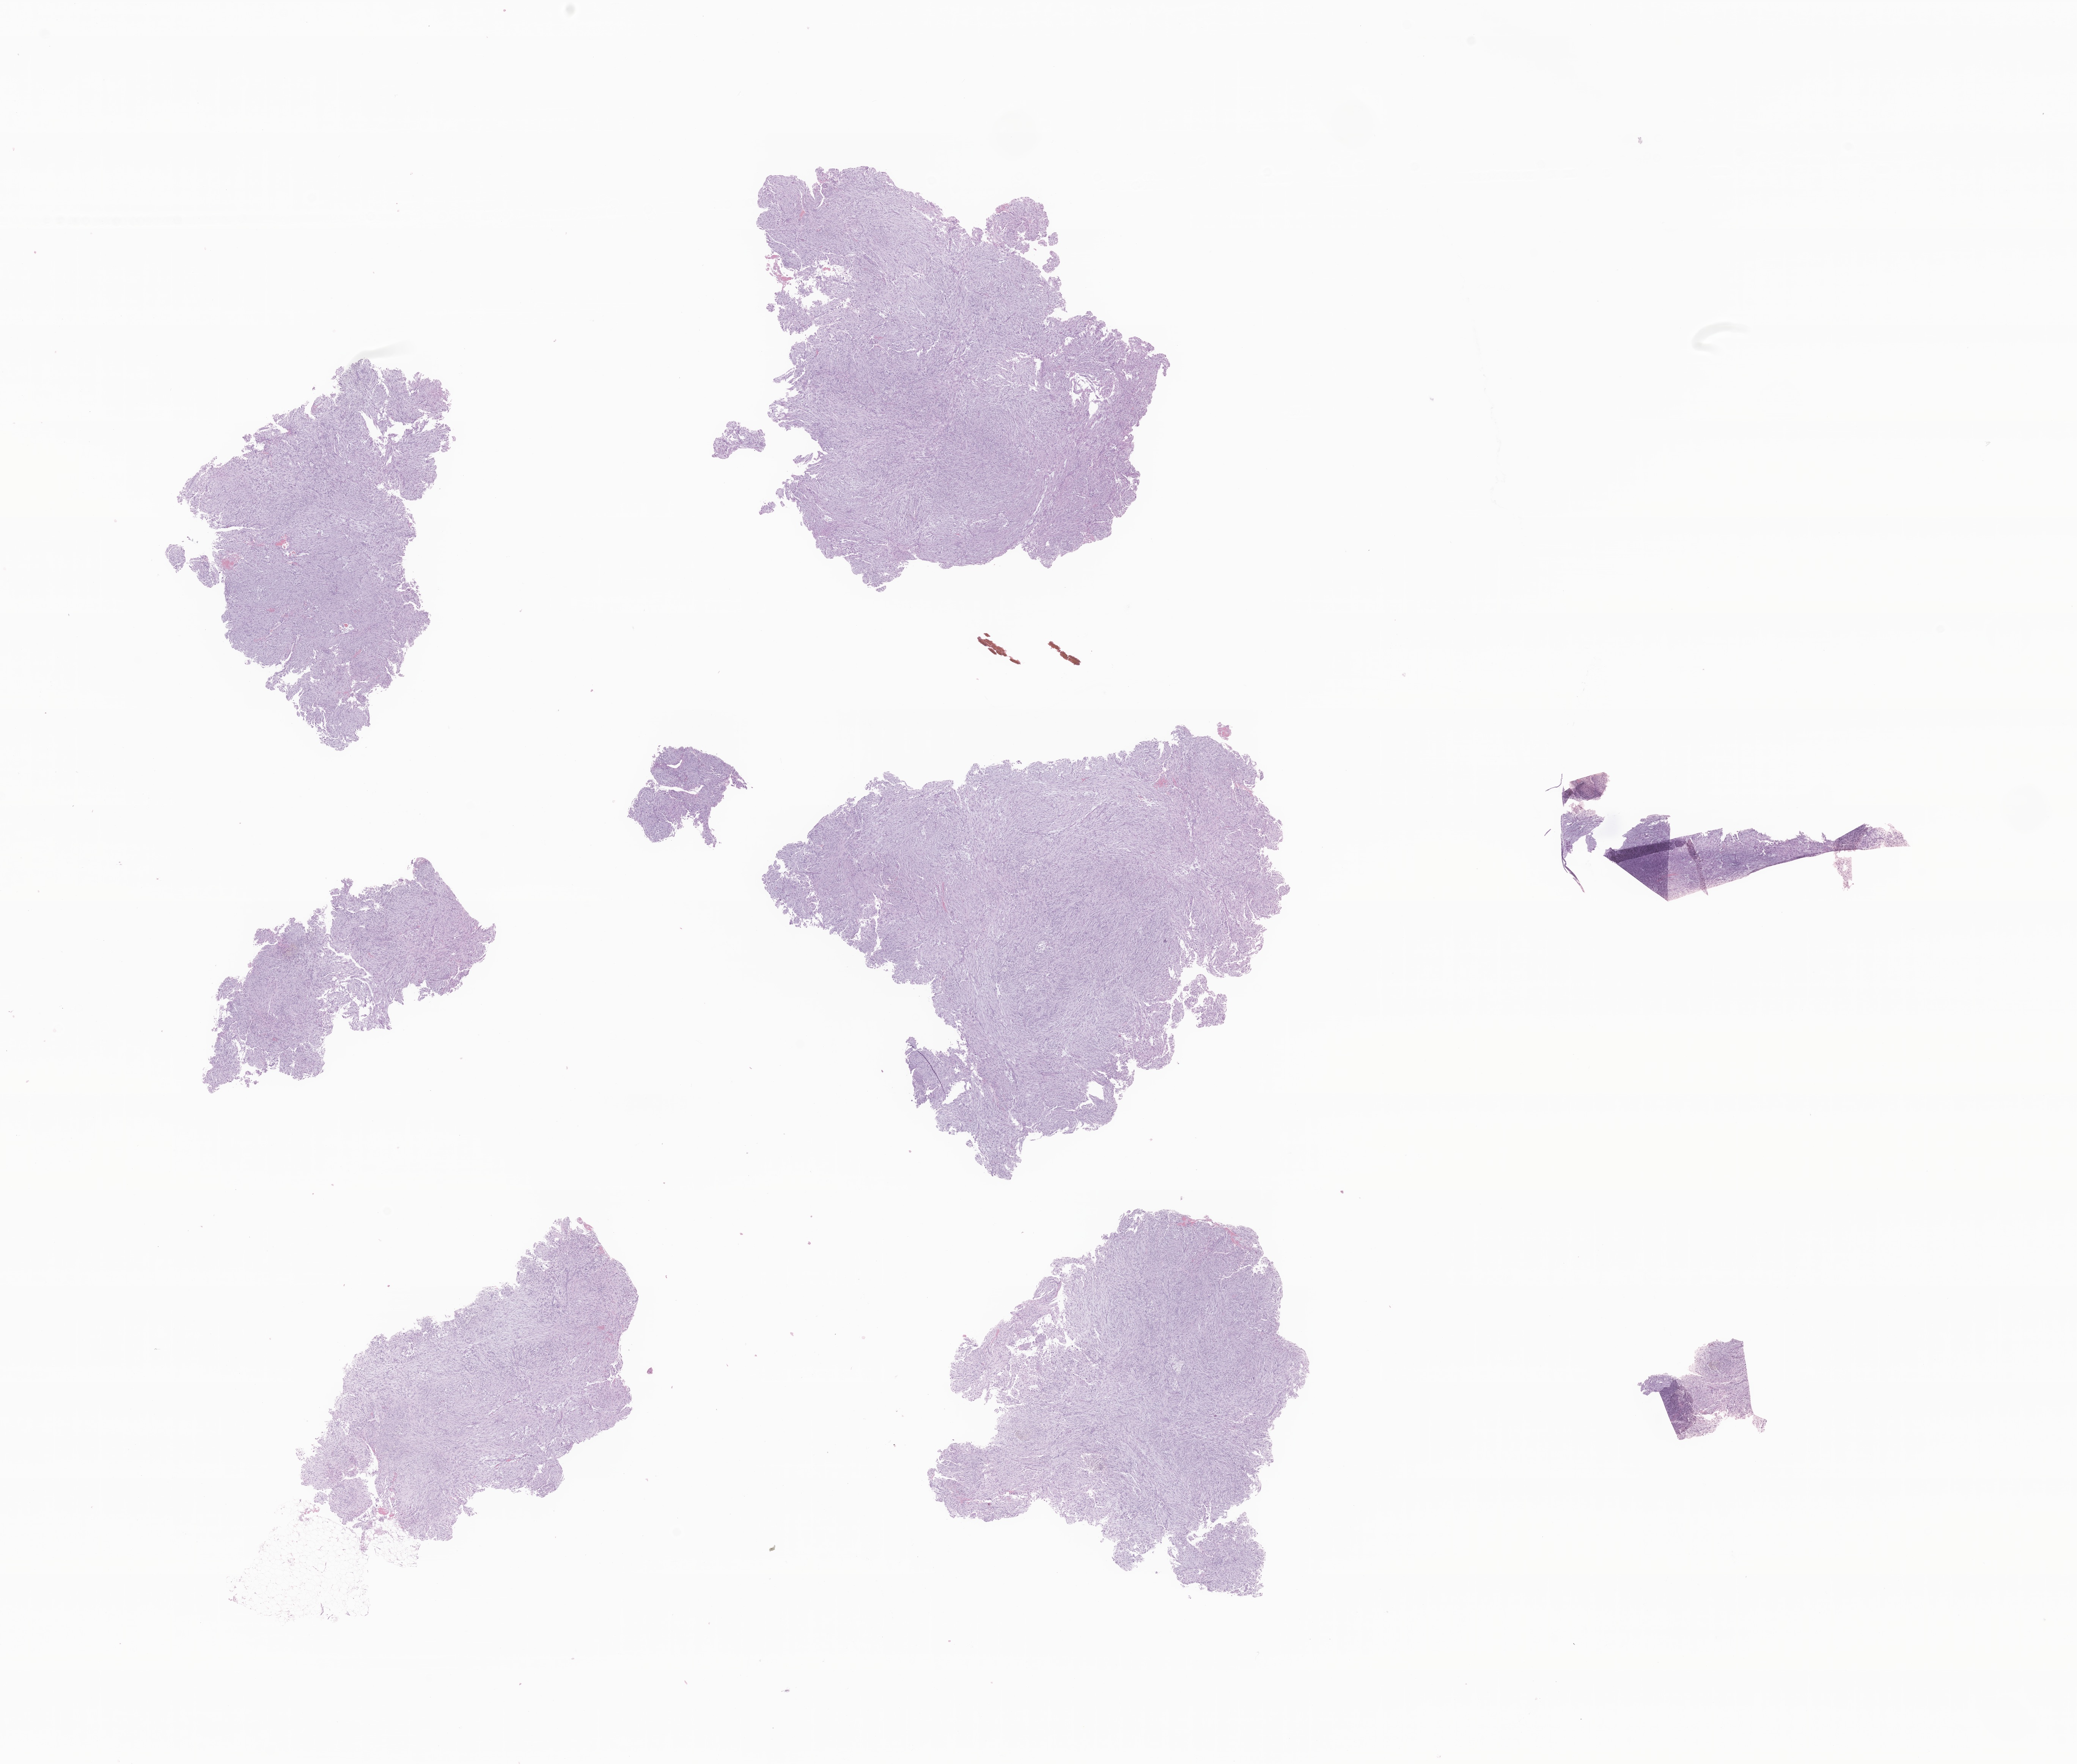
Haematoxylin and eosin whole-slide image of tumor tissue from the lower limb lymph node — shown as a low-resolution overview of the whole scanned area (about 23.1 x 19.6 mm), FFPE section. Male patient, age 82 months (6 years 10 months).
Diagnosis (ICD-O-3 morphology term): Myofibromatosis.